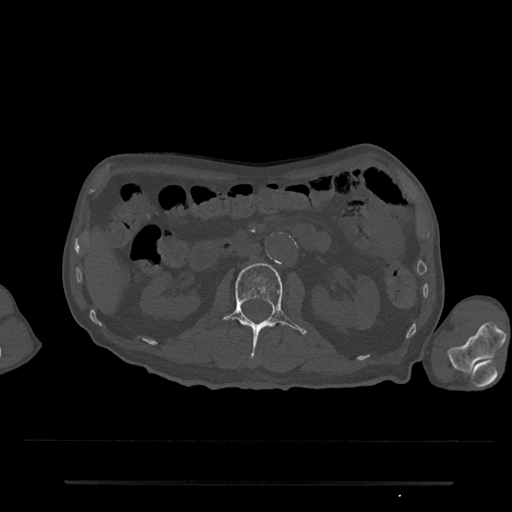
CT including the spine, one axial slice; slice 64 of 797 in the series (ordered by position); 120 kVp; bone window (W 1800 / L 400 HU); 512 × 512 image matrix. Patient: male, 74 years. From the clinical record (not read from this slice): primary cancer: prostate.
Outlined on this slice (semi-automatic segmentation, software-assisted and operator-edited):
- L2 vertebra: bounding box [x1, y1, x2, y2] px = [210, 263, 307, 346]